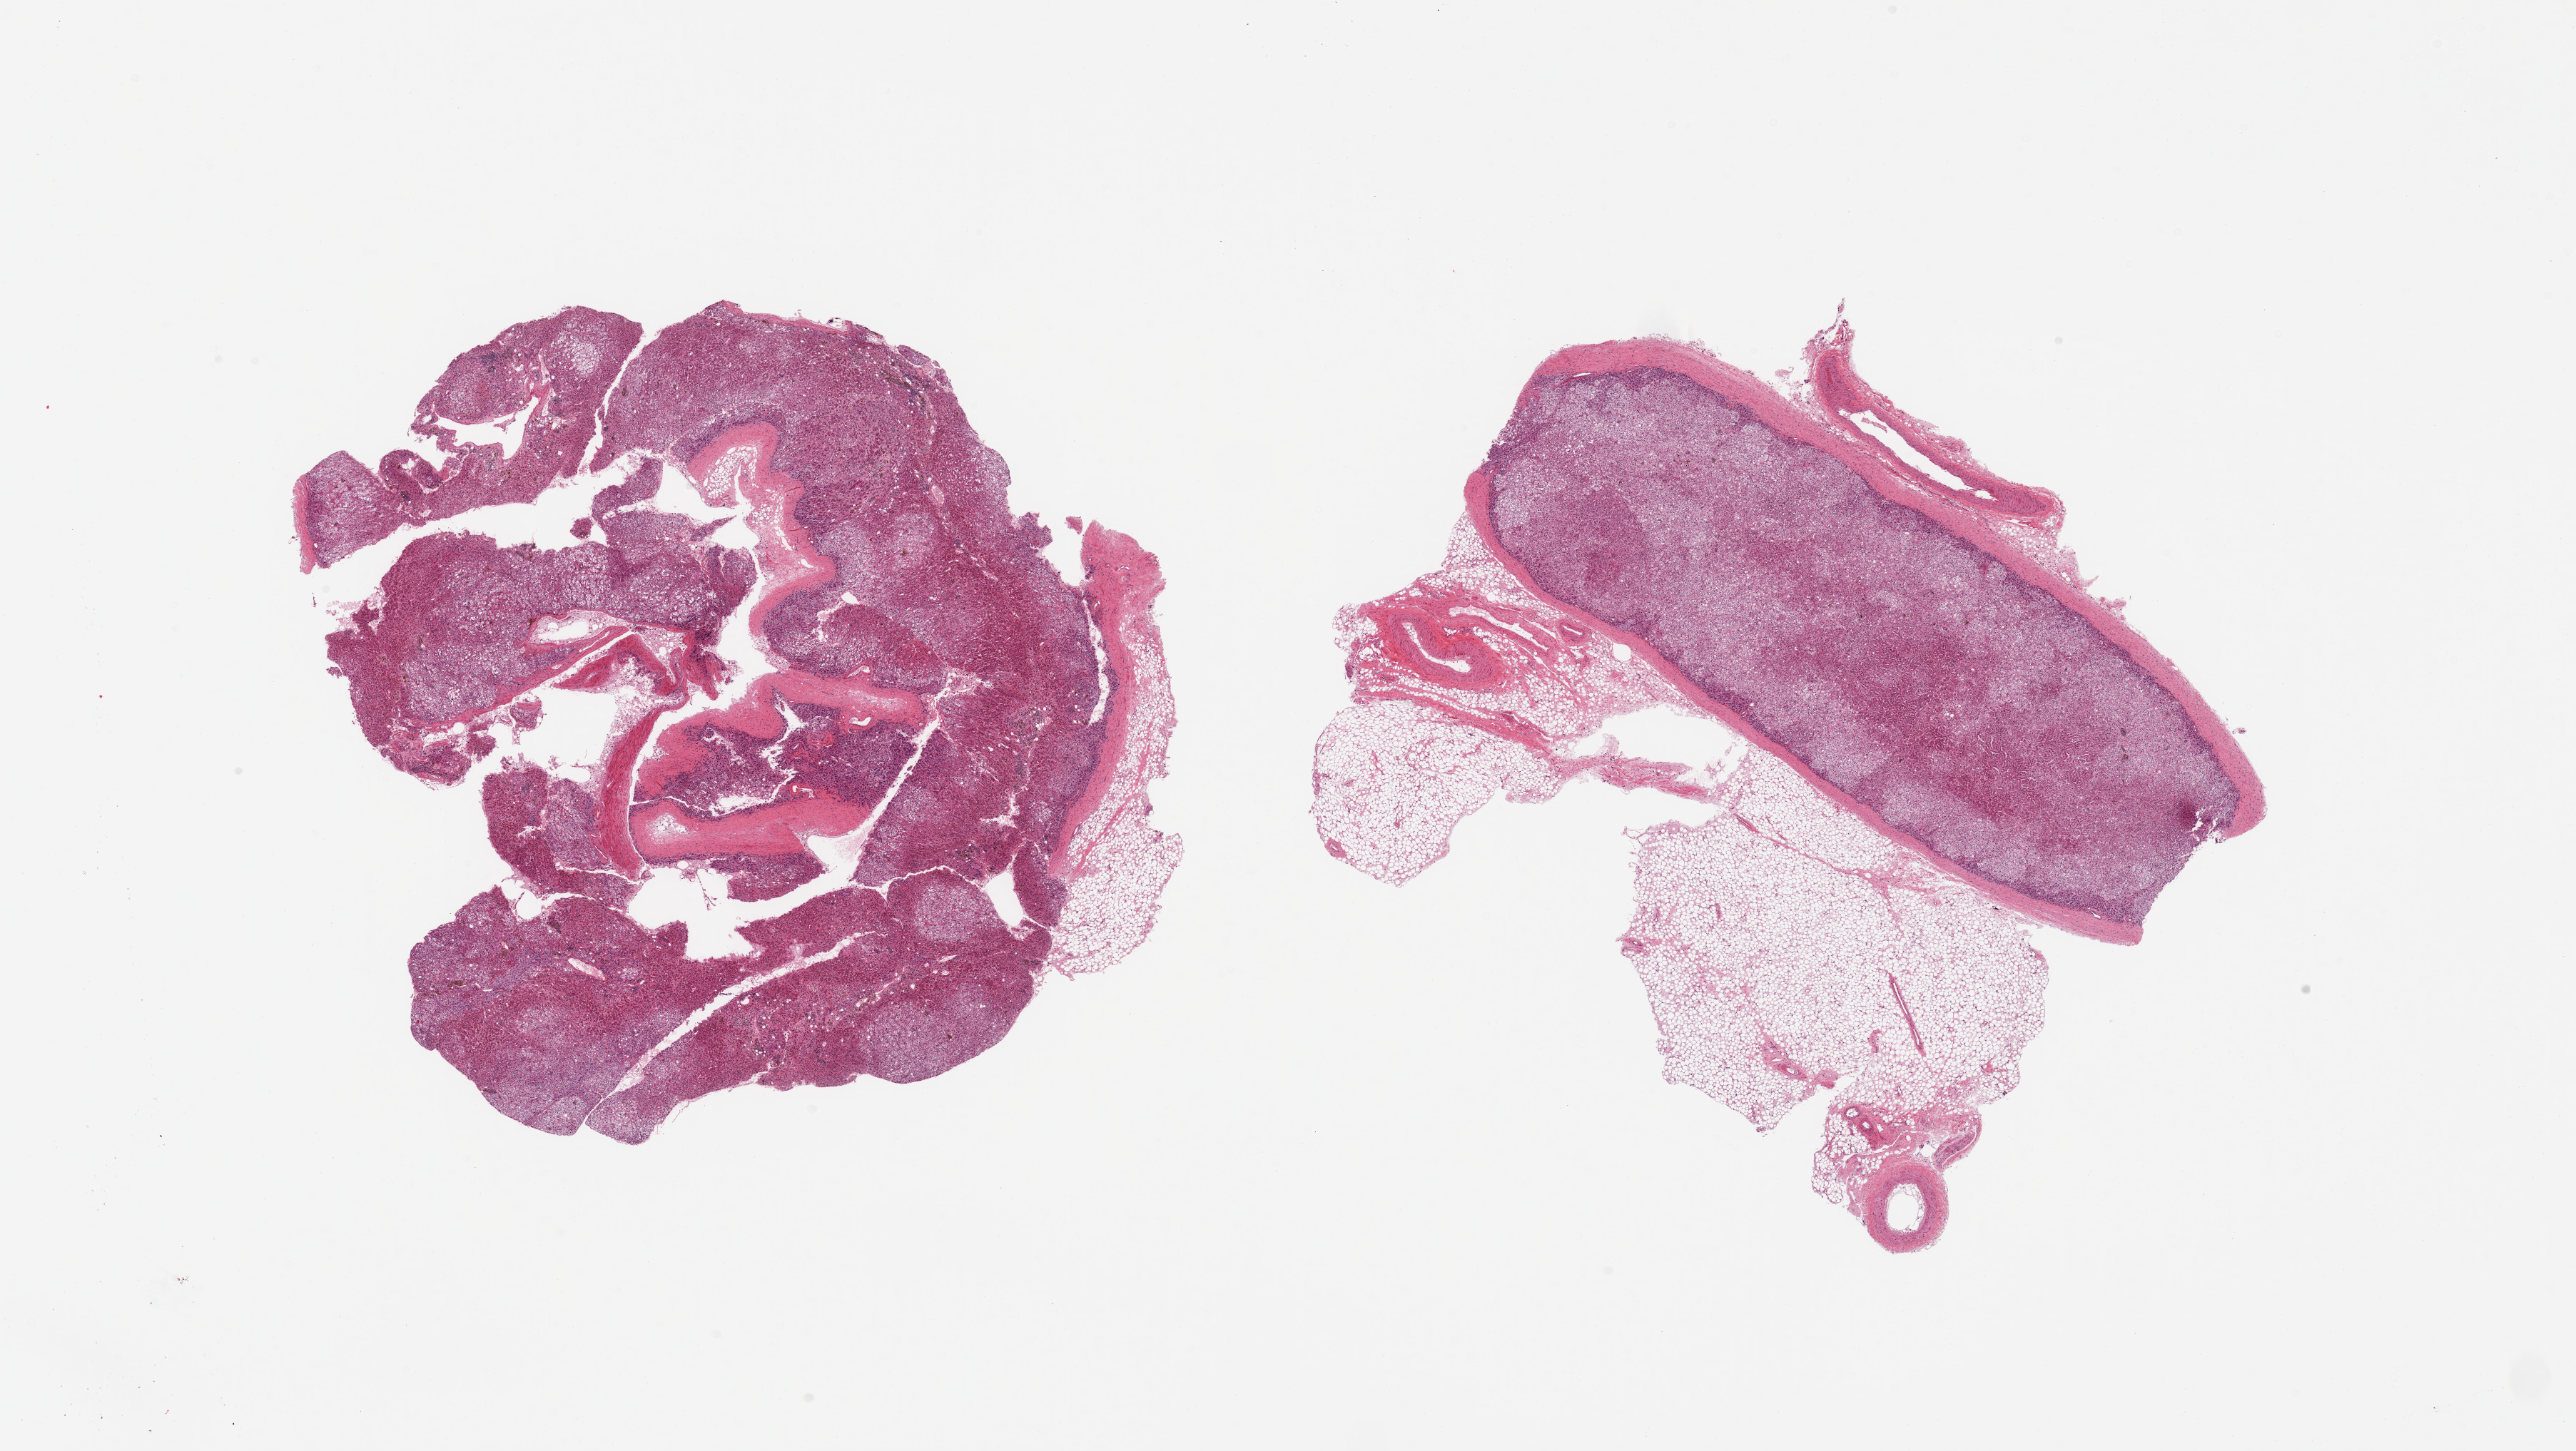
Hematoxylin and eosin (H&E) whole-slide image, low-resolution overview of the scanned area, about 28.5 x 16.1 mm; PAXgene-fixed paraffin-embedded (PFPE) section; sampled site (target tissue): adrenal gland; tissue donor sample. Male donor.
Pathologist's review note for this sample: 2 pieces; all cortex; 1 piece has 50% external fat.